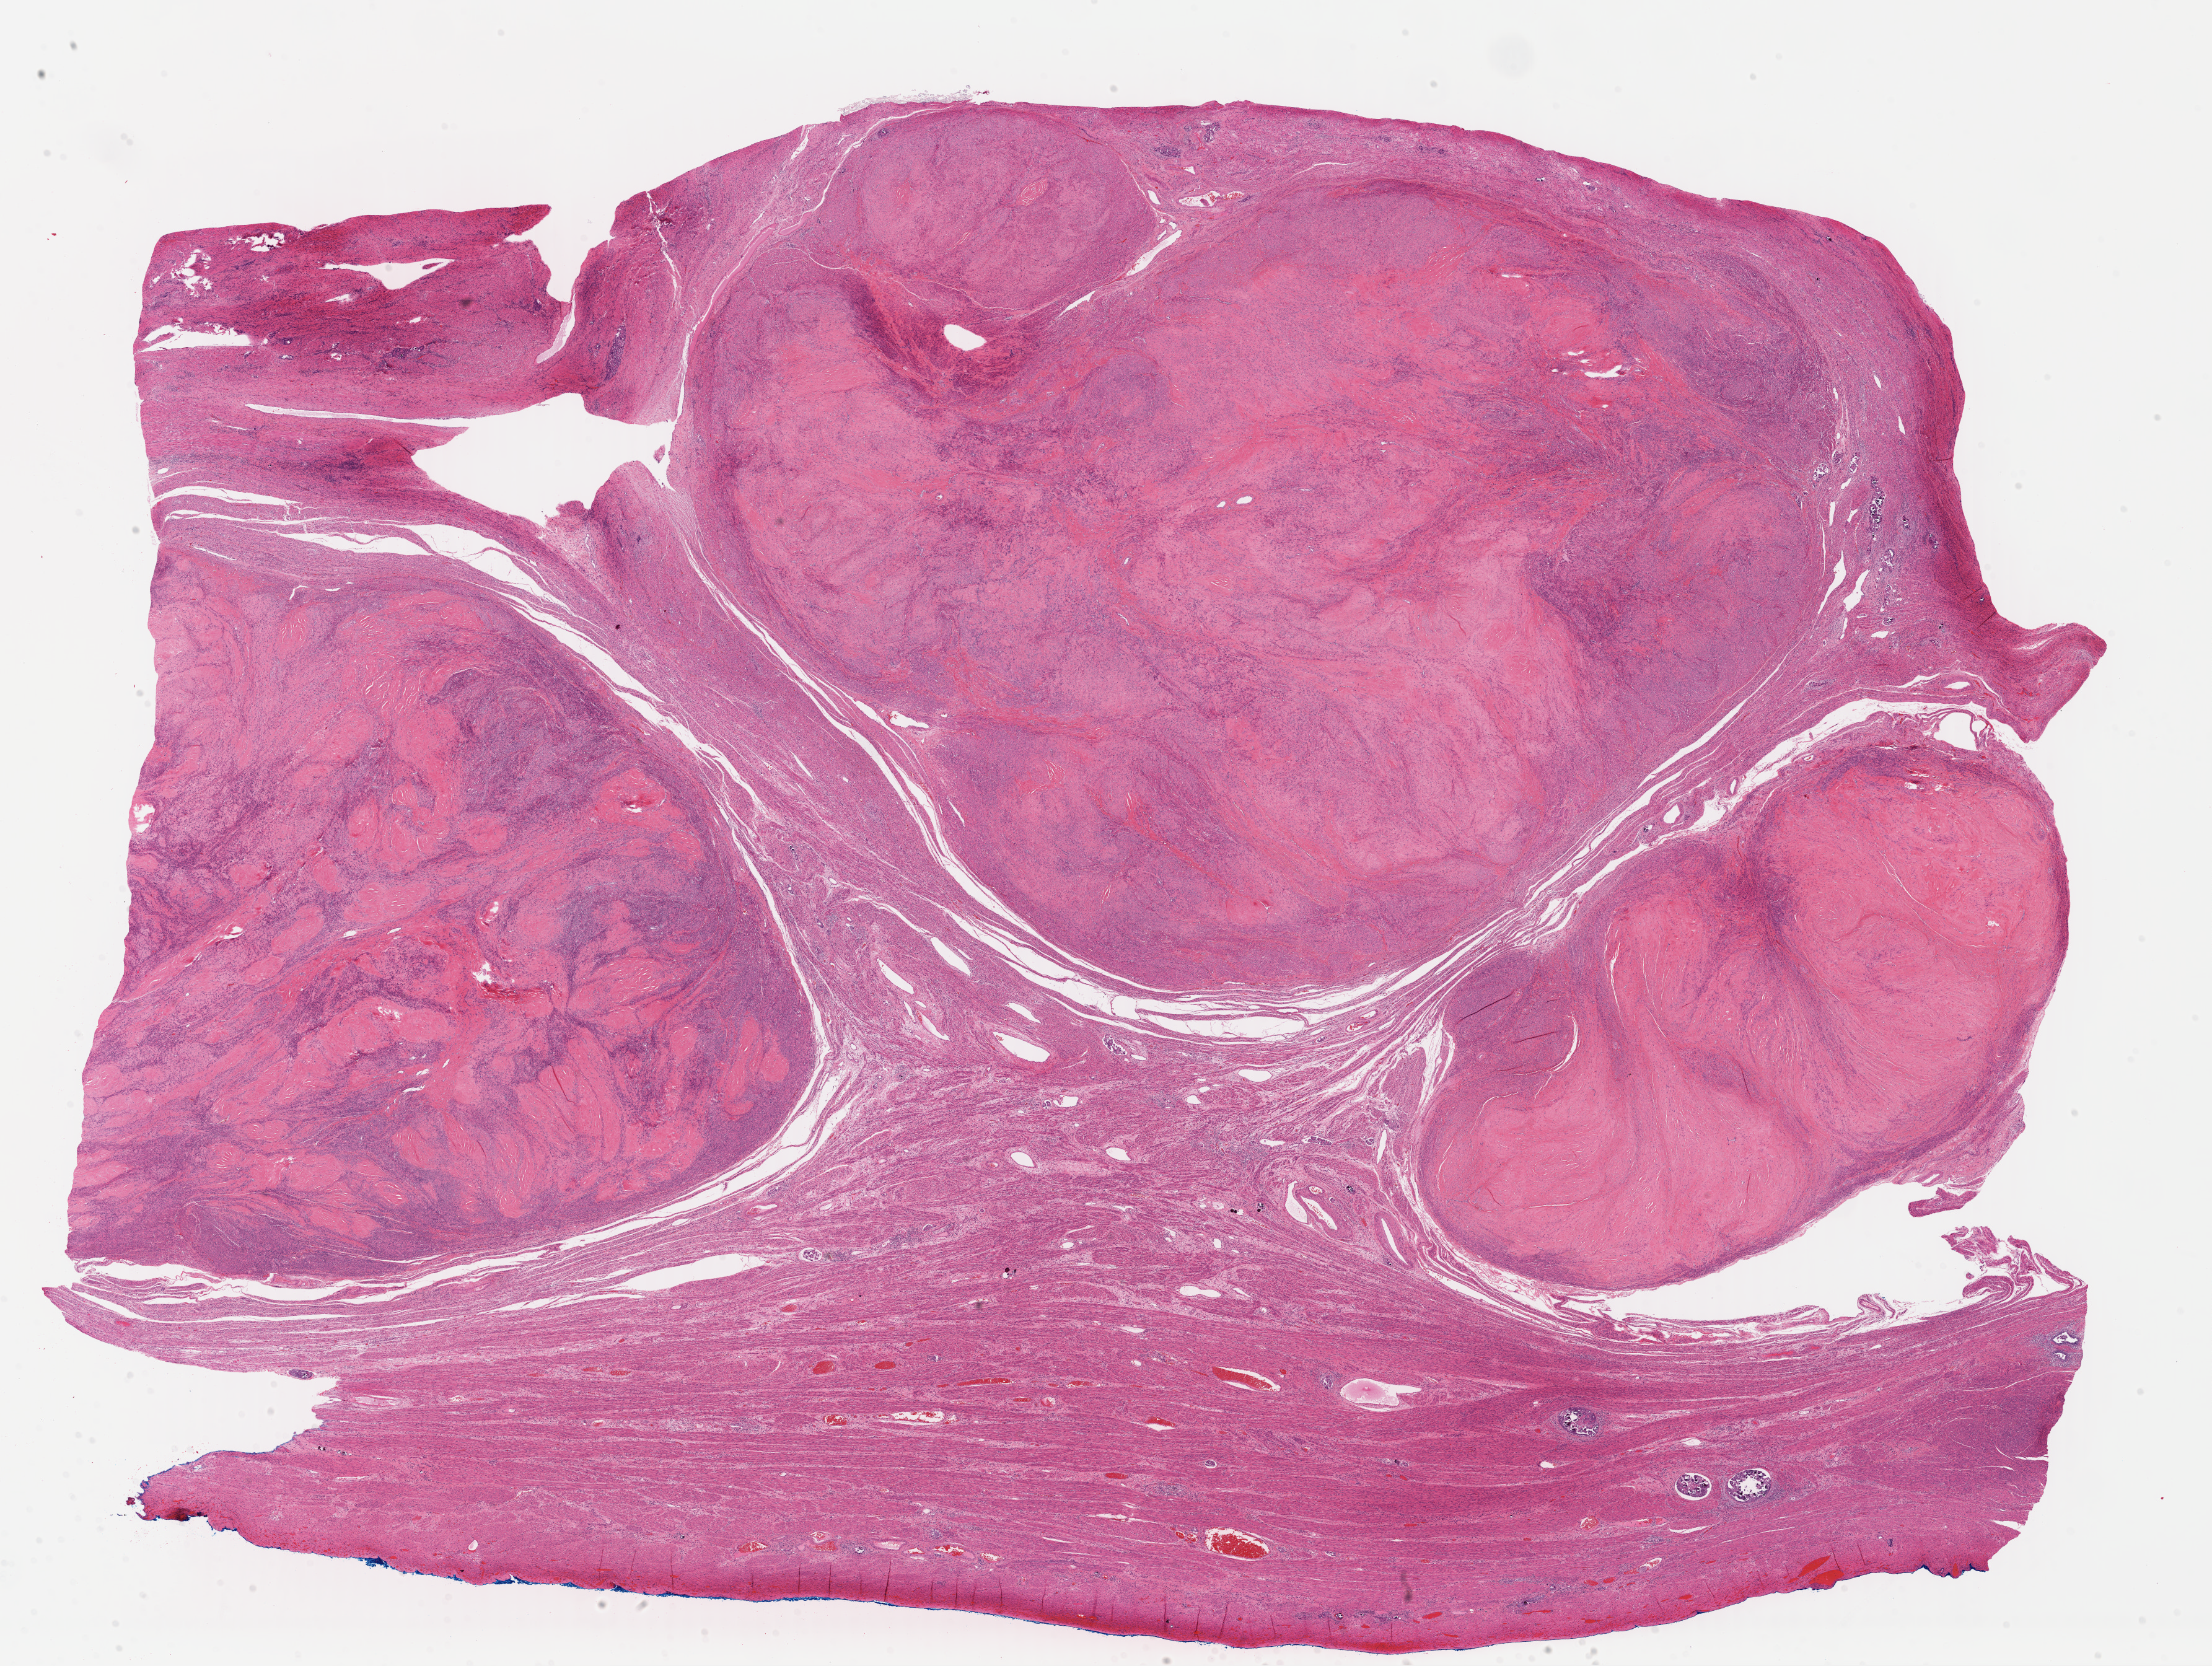
H&E-stained whole-slide image — low-resolution overview of the scanned area, about 28.1 x 21.1 mm; formalin-fixed paraffin-embedded (FFPE) diagnostic section; uterus, primary tumour sample. Female, age 67 years at initial diagnosis.
Histologic diagnosis: Mullerian mixed tumor. FIGO stage: IIIC.